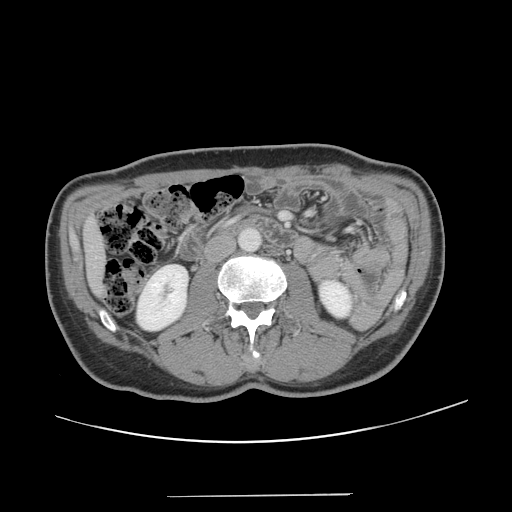
Contrast-enhanced abdominal CT, one axial slice. Slice 43 of 131 in the series (ordered by position). Soft-tissue window (W 400 / L 40 HU). 2.5 mm slice thickness. 512 × 512 image matrix, field of view 403 × 403 mm. Male patient, age 60 years. Case-level facts recorded for this patient, not image findings: diagnosis: colorectal cancer liver metastases, imaged before liver resection; multiple liver metastases: no; largest metastasis: 2.5 cm; disease in both lobes: no.
Outlined on this slice (manually delineated by an expert):
- liver: bounding box (x1, y1, x2, y2) in pixels: (85, 222, 104, 294)
- planned liver remnant (the part of the liver to remain after resection): (85, 222, 104, 294)